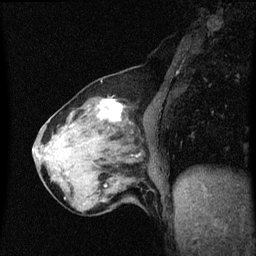
Breast MRI (dynamic contrast-enhanced), one sagittal slice; slice 22 of 60 in the series (ordered by position); dynamic contrast-enhanced series, image 2 of 3 at this slice position (ordered by acquisition); 1.5 T; TE 4.2 ms, TR 8.4 ms; 2 mm slice thickness; 256 × 256 image matrix, field of view 200 × 200 mm. Female patient, age 64 years. From the clinical record (not read from this slice): setting: breast cancer imaged before/during neoadjuvant chemotherapy; receptor status: HR-positive, HER2-negative.
Annotated regions visible in this slice (semi-automatic segmentation, software-assisted and operator-edited):
- analysis volume of interest (the breast-tissue region the enhancement analysis was run in; not a lesion): bounding box (x1, y1, x2, y2) in pixels: (56, 100, 139, 175)
- tumour enhancement mask (voxels above the 70 % enhancement threshold inside the analysis volume of interest): (103, 100, 124, 121)